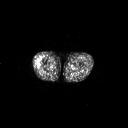
FDG PET of an extremity soft-tissue mass (from a PET/CT study), one axial slice. Slice 221 of 267 in the series (ordered by position). 3.27 mm slice thickness. 128 × 128 image matrix, field of view 700 × 700 mm. Male patient, age 43 years. From the clinical record (not read from this slice): histological type: poorly differentiated synovial sarcoma; grade: high; site of the primary tumour: right buttock.
Annotated regions visible in this slice (expert contour drawn on MRI and transferred to this co-registered scan by the dataset authors):
- gross tumour volume including surrounding oedema: bounding box (x1, y1, x2, y2) in pixels: (36, 60, 43, 67)